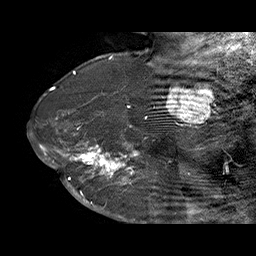
Breast MRI (dynamic contrast-enhanced), one sagittal slice. Slice 48 of 70 in the series (ordered by position). Dynamic contrast-enhanced series, time point 2 of 6 at this slice position (early post-contrast). 1.5 T. TE 4.5 ms, TR 32.4 ms. 3 mm slice thickness. 256 × 256 image matrix, field of view 180 × 180 mm. Female patient. From the clinical record (not read from this slice): setting: breast cancer imaged before/during neoadjuvant chemotherapy; receptor status: HR-positive, HER2-negative.
Outlined on this slice (semi-automatic segmentation, software-assisted and operator-edited):
- analysis volume of interest (the breast-tissue region the enhancement analysis was run in; not a lesion): bounding box (x1, y1, x2, y2) in pixels: (71, 128, 159, 202)
- tumour enhancement mask (voxels above the 100 % enhancement threshold inside the analysis volume of interest): (71, 128, 155, 202)